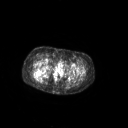
FDG PET of an extremity soft-tissue mass (from a PET/CT study), one axial slice. Slice 60 of 267 in the series (ordered by position). 3.27 mm slice thickness. 128 × 128 image matrix, field of view 700 × 700 mm. Patient: female, 70 years. Case-level facts recorded for this patient, not image findings: histological type: synovial sarcoma; grade: intermediate; site of the primary tumour: right buttock.
Annotated regions visible in this slice (expert contour drawn on MRI and transferred to this co-registered scan by the dataset authors):
- gross tumour volume including surrounding oedema: bounding box (x1, y1, x2, y2) in pixels: (33, 69, 46, 80)
- gross tumour volume (mass): (33, 69, 42, 76)